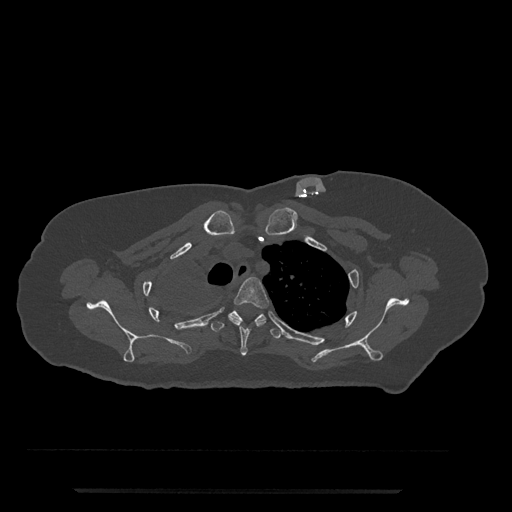
CT including the spine, one axial slice; position 617 of 797 along the scan axis; 120 kVp; bone window (W 1800 / L 400 HU); 512 × 512 image matrix, field of view 440 × 440 mm. Patient: female, 51 years. Case-level facts recorded for this patient, not image findings: primary cancer: neuro.
Outlined on this slice (semi-automatically segmented with operator editing):
- T3 vertebra: box from (x=228, y=277) to (x=270, y=356) px
- T4 vertebra: (x=211, y=310)–(x=282, y=339)